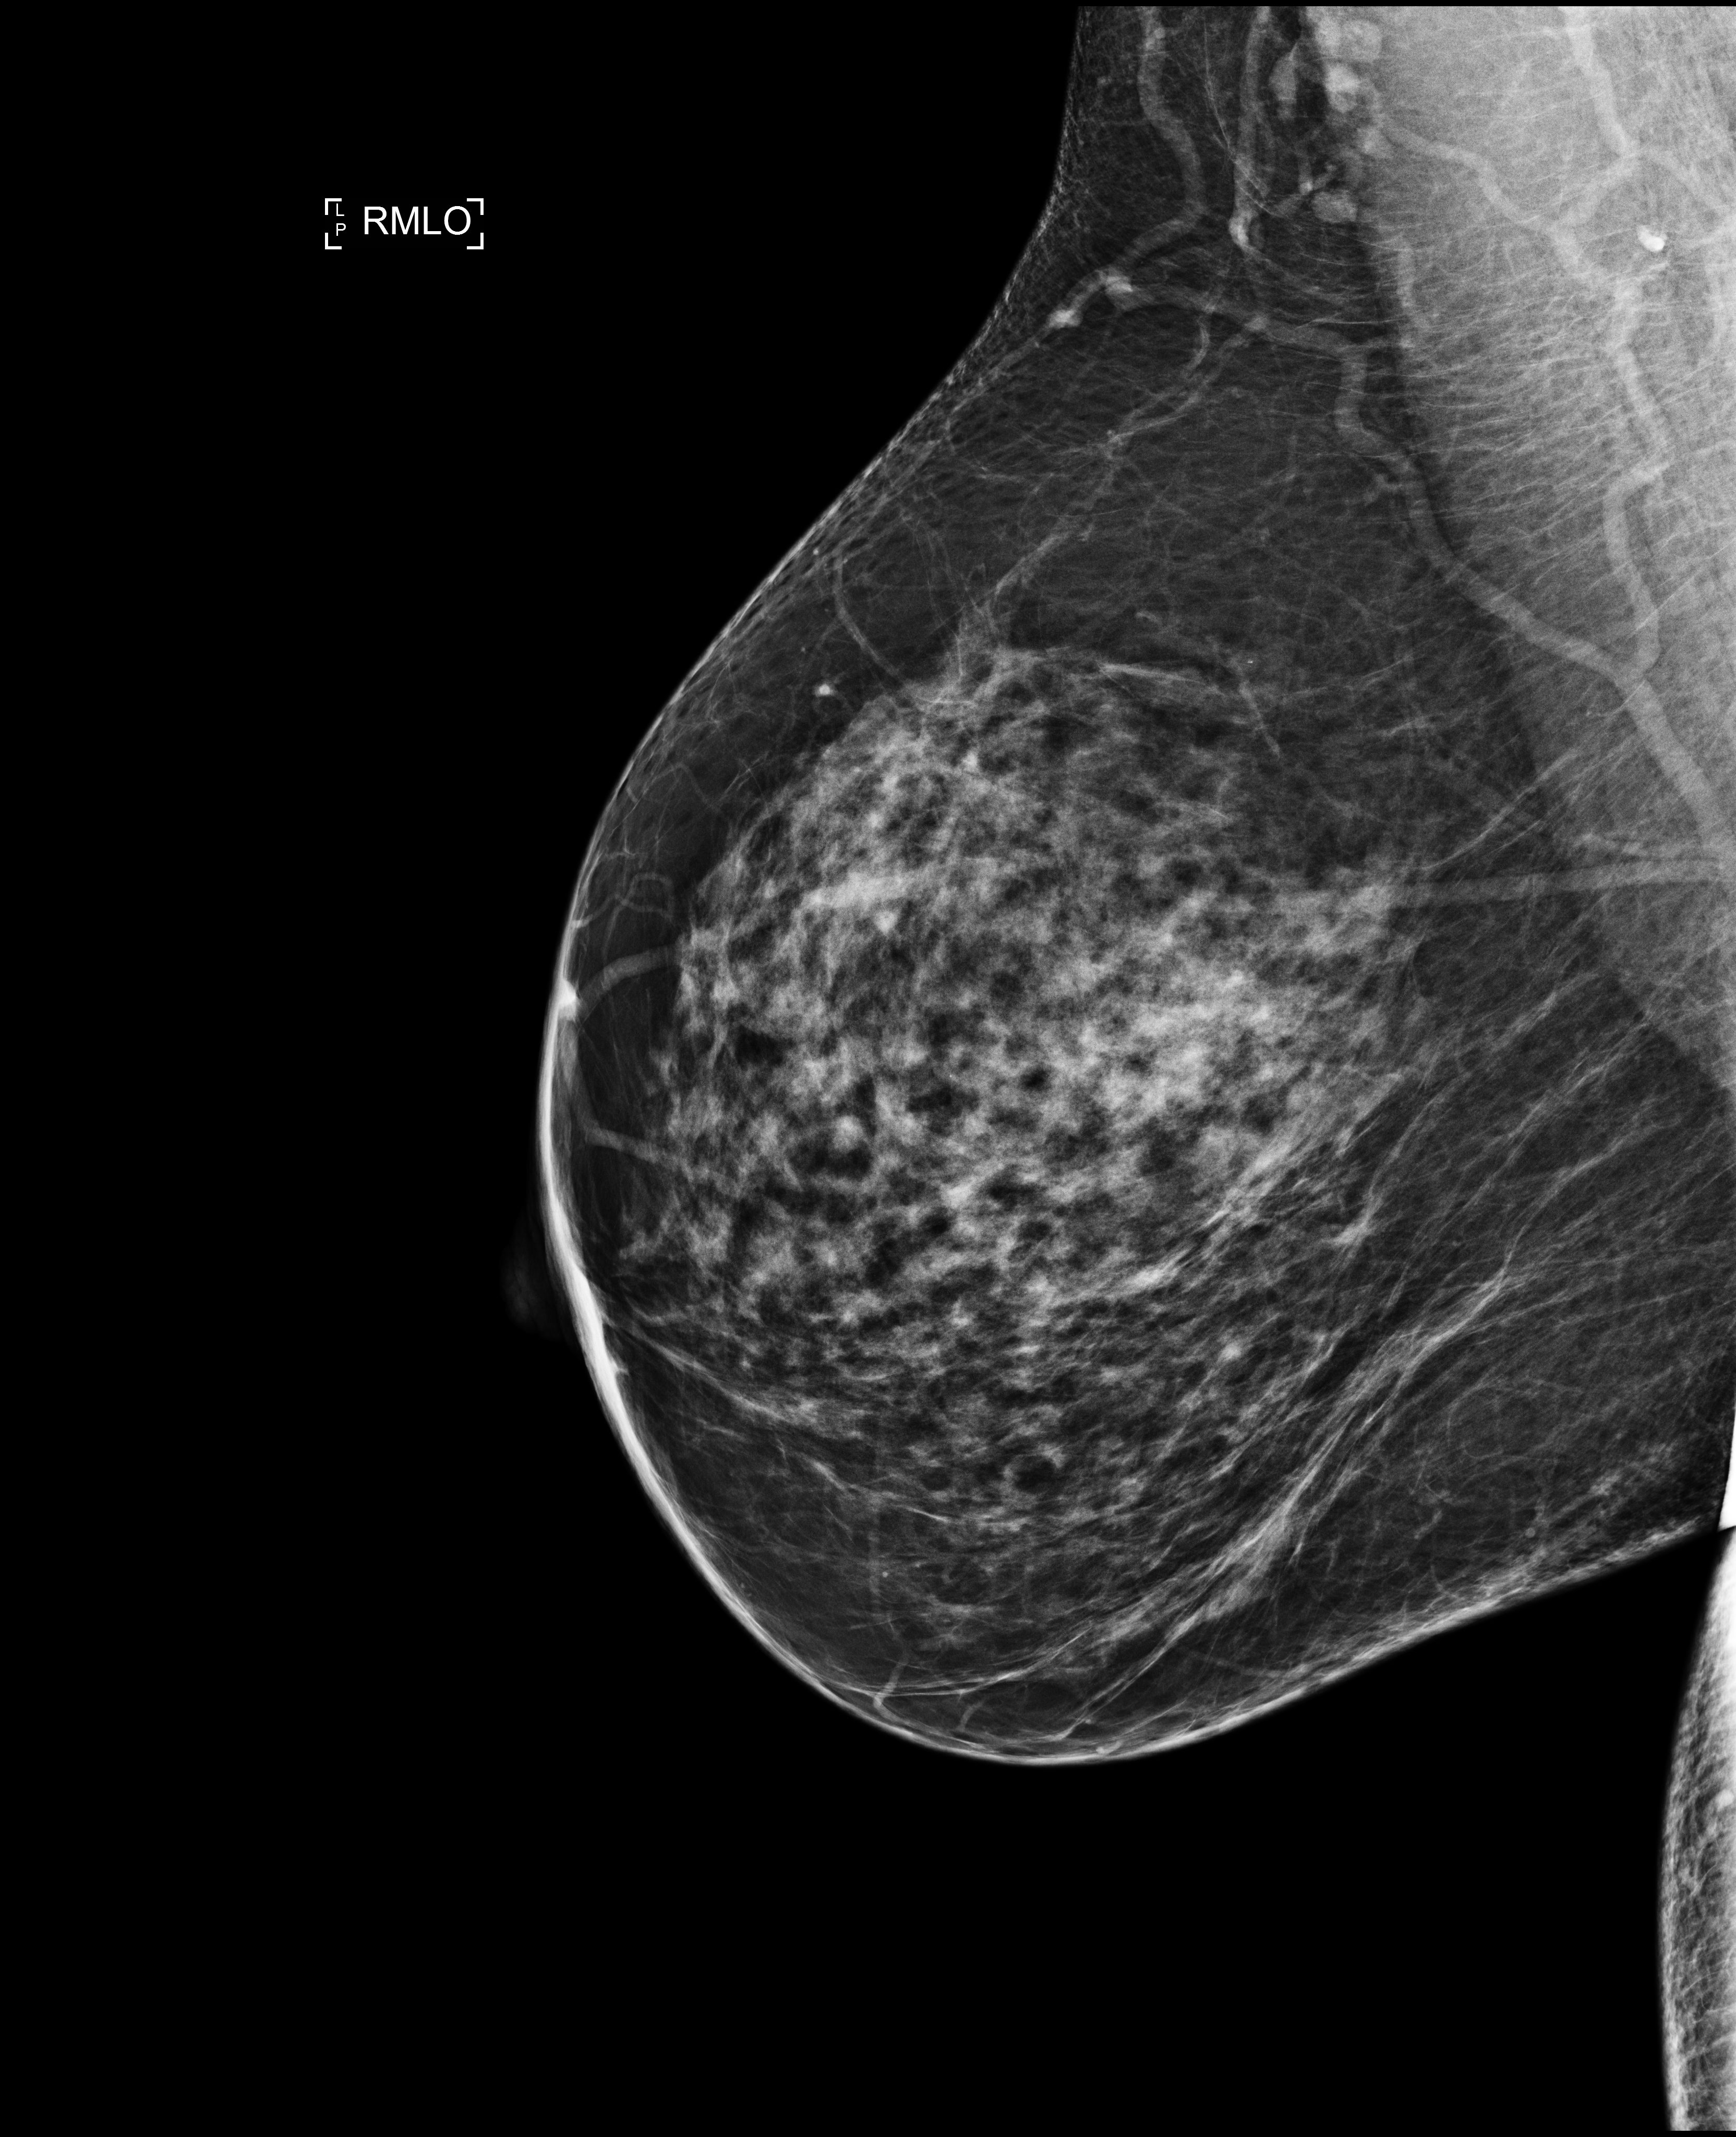
Digital mammogram (FFDM), right breast, medio-lateral oblique projection, annual screening mammography examination, system: Selenia Dimensions. Female patient, age 50 years.
- BI-RADS breast density category at the screening exam (both breasts, scale 1–4): 3
- final BI-RADS category for the screening round (tomosynthesis exam, both breasts): category 1
- recall: no recall after this screen